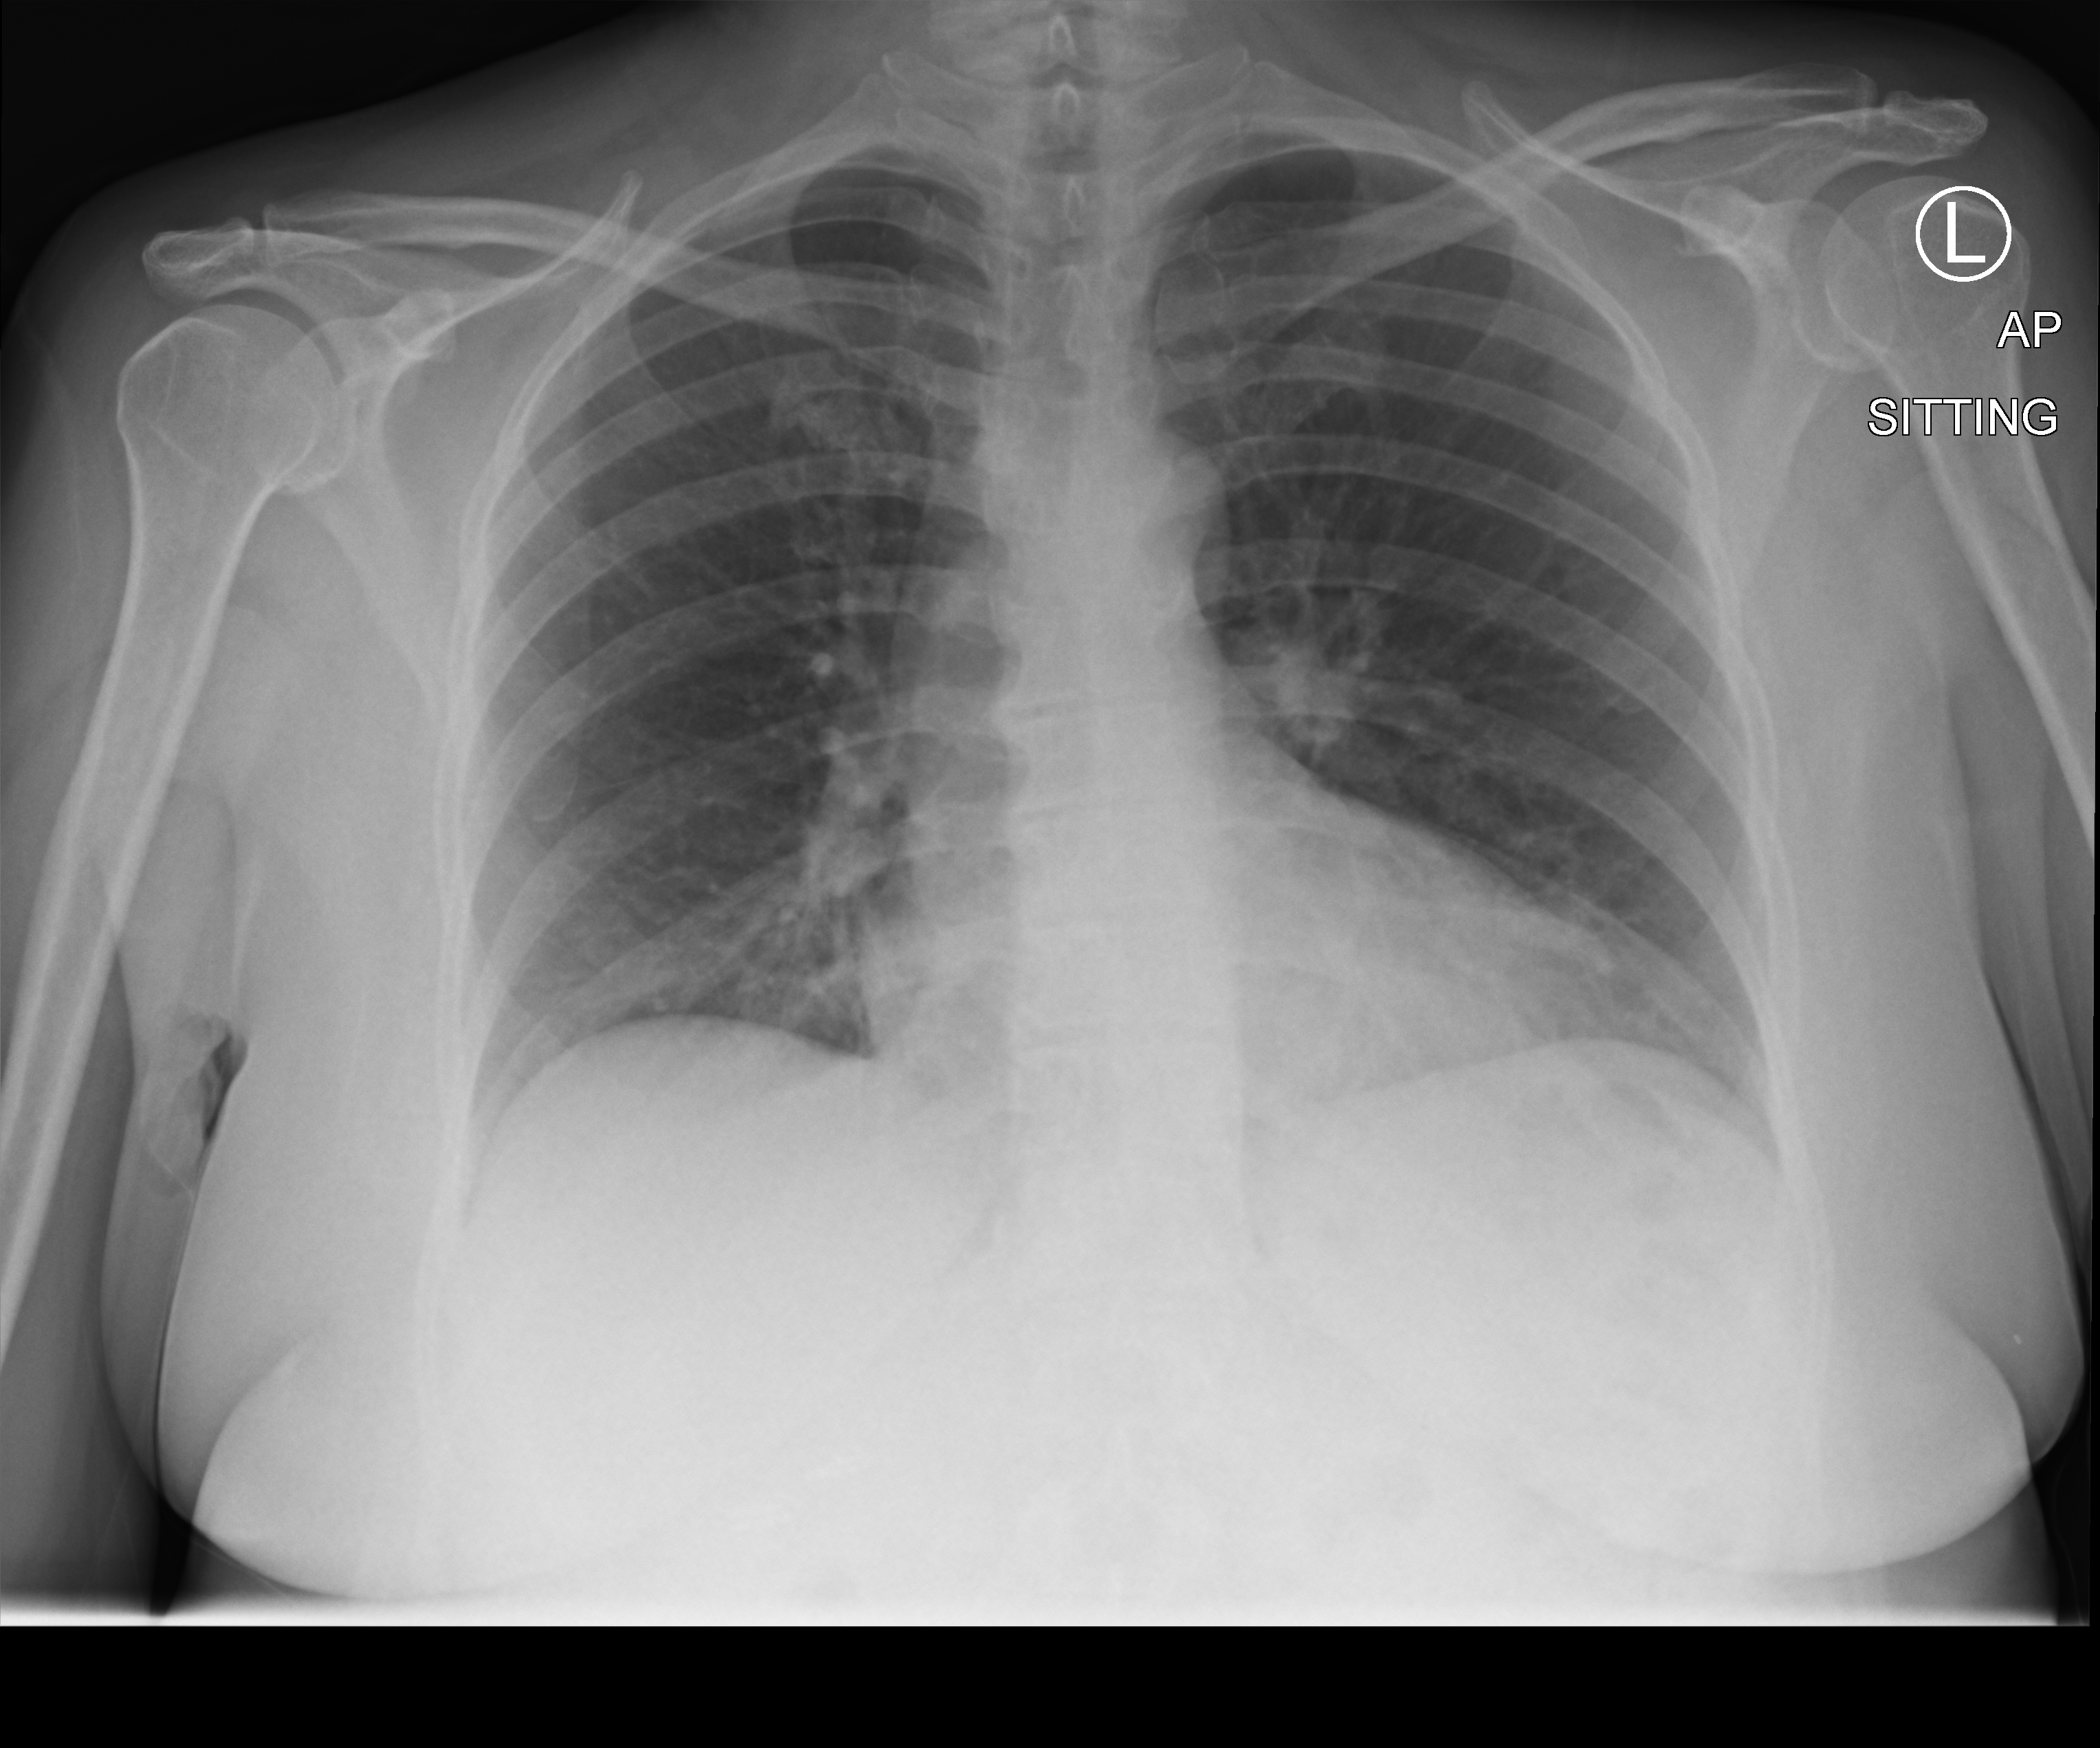
Bedside chest radiograph (computed radiography); anteroposterior (AP) projection. Patient hospitalised with COVID-19; female, aged 18–59 years.
Hospital-stay facts (about this admission, not read from this image; timing relative to this image not recorded): mechanically ventilated during this hospital stay: no; chronic kidney disease (admission record): no; admitted to intensive care during this hospital stay: no.